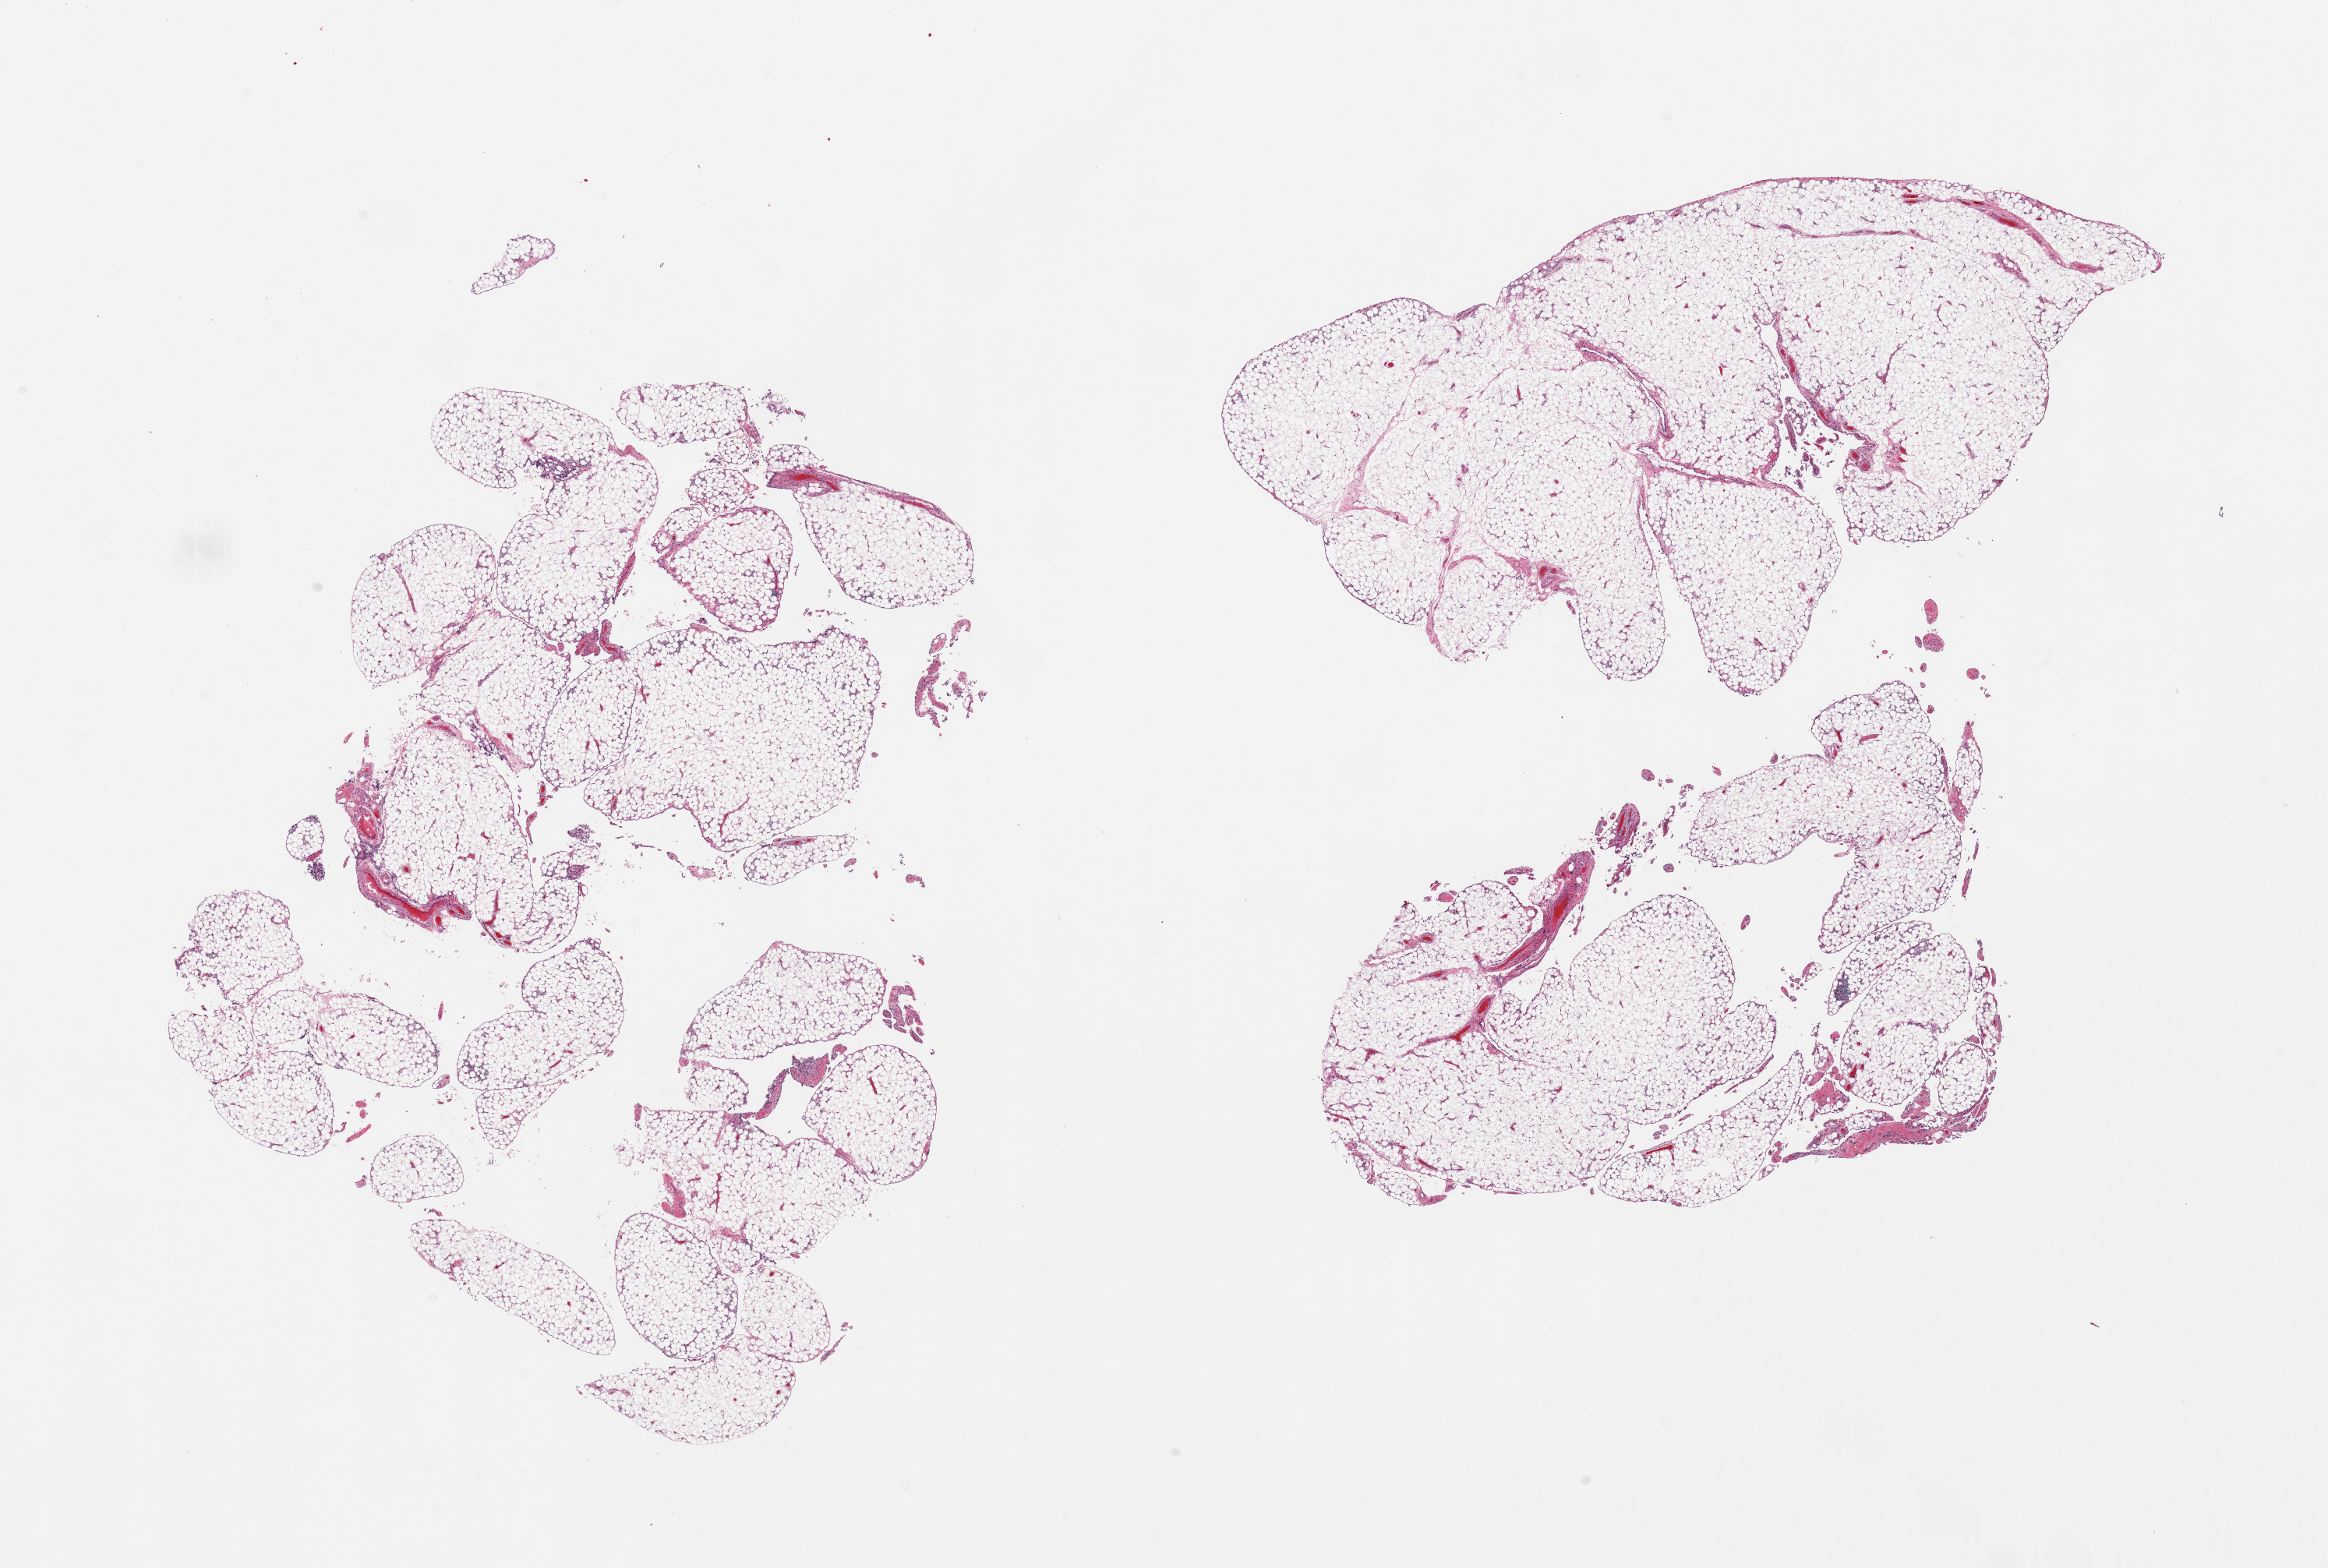
Haematoxylin and eosin whole-slide image, brightfield, low-resolution overview of the scanned area, about 23.6 x 15.9 mm, PAXgene-fixed paraffin-embedded (PFPE) section, section of omentum (target tissue), tissue donor sample. Donor: female.
Reviewer comment on this tissue sample: 2 pieces; lobulated mature fat, clusters of reactive mesothelial cells, mild chronic inflammation.